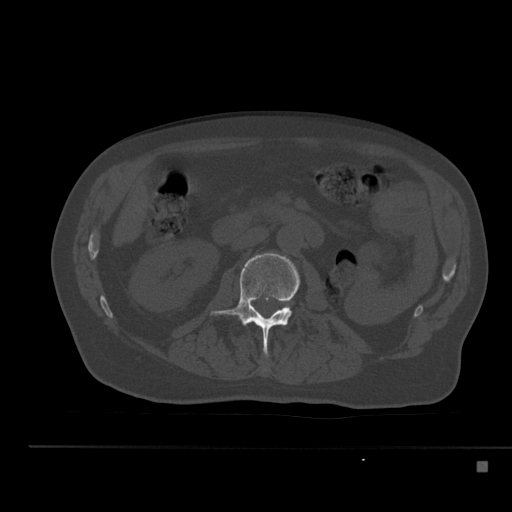
CT including the spine, one axial slice. Slice 185 of 517 in the series (ordered by position). Bone window (W 1800 / L 400 HU). 1.5 mm slice thickness. 512 × 512 image matrix, field of view 408 × 408 mm. Patient: male, 70 years. From the clinical record (not read from this slice): primary cancer: renal.
Structures marked on this image (semi-automatic segmentation, software-assisted and operator-edited):
- L2 vertebra: box from (x=210, y=253) to (x=299, y=355) px